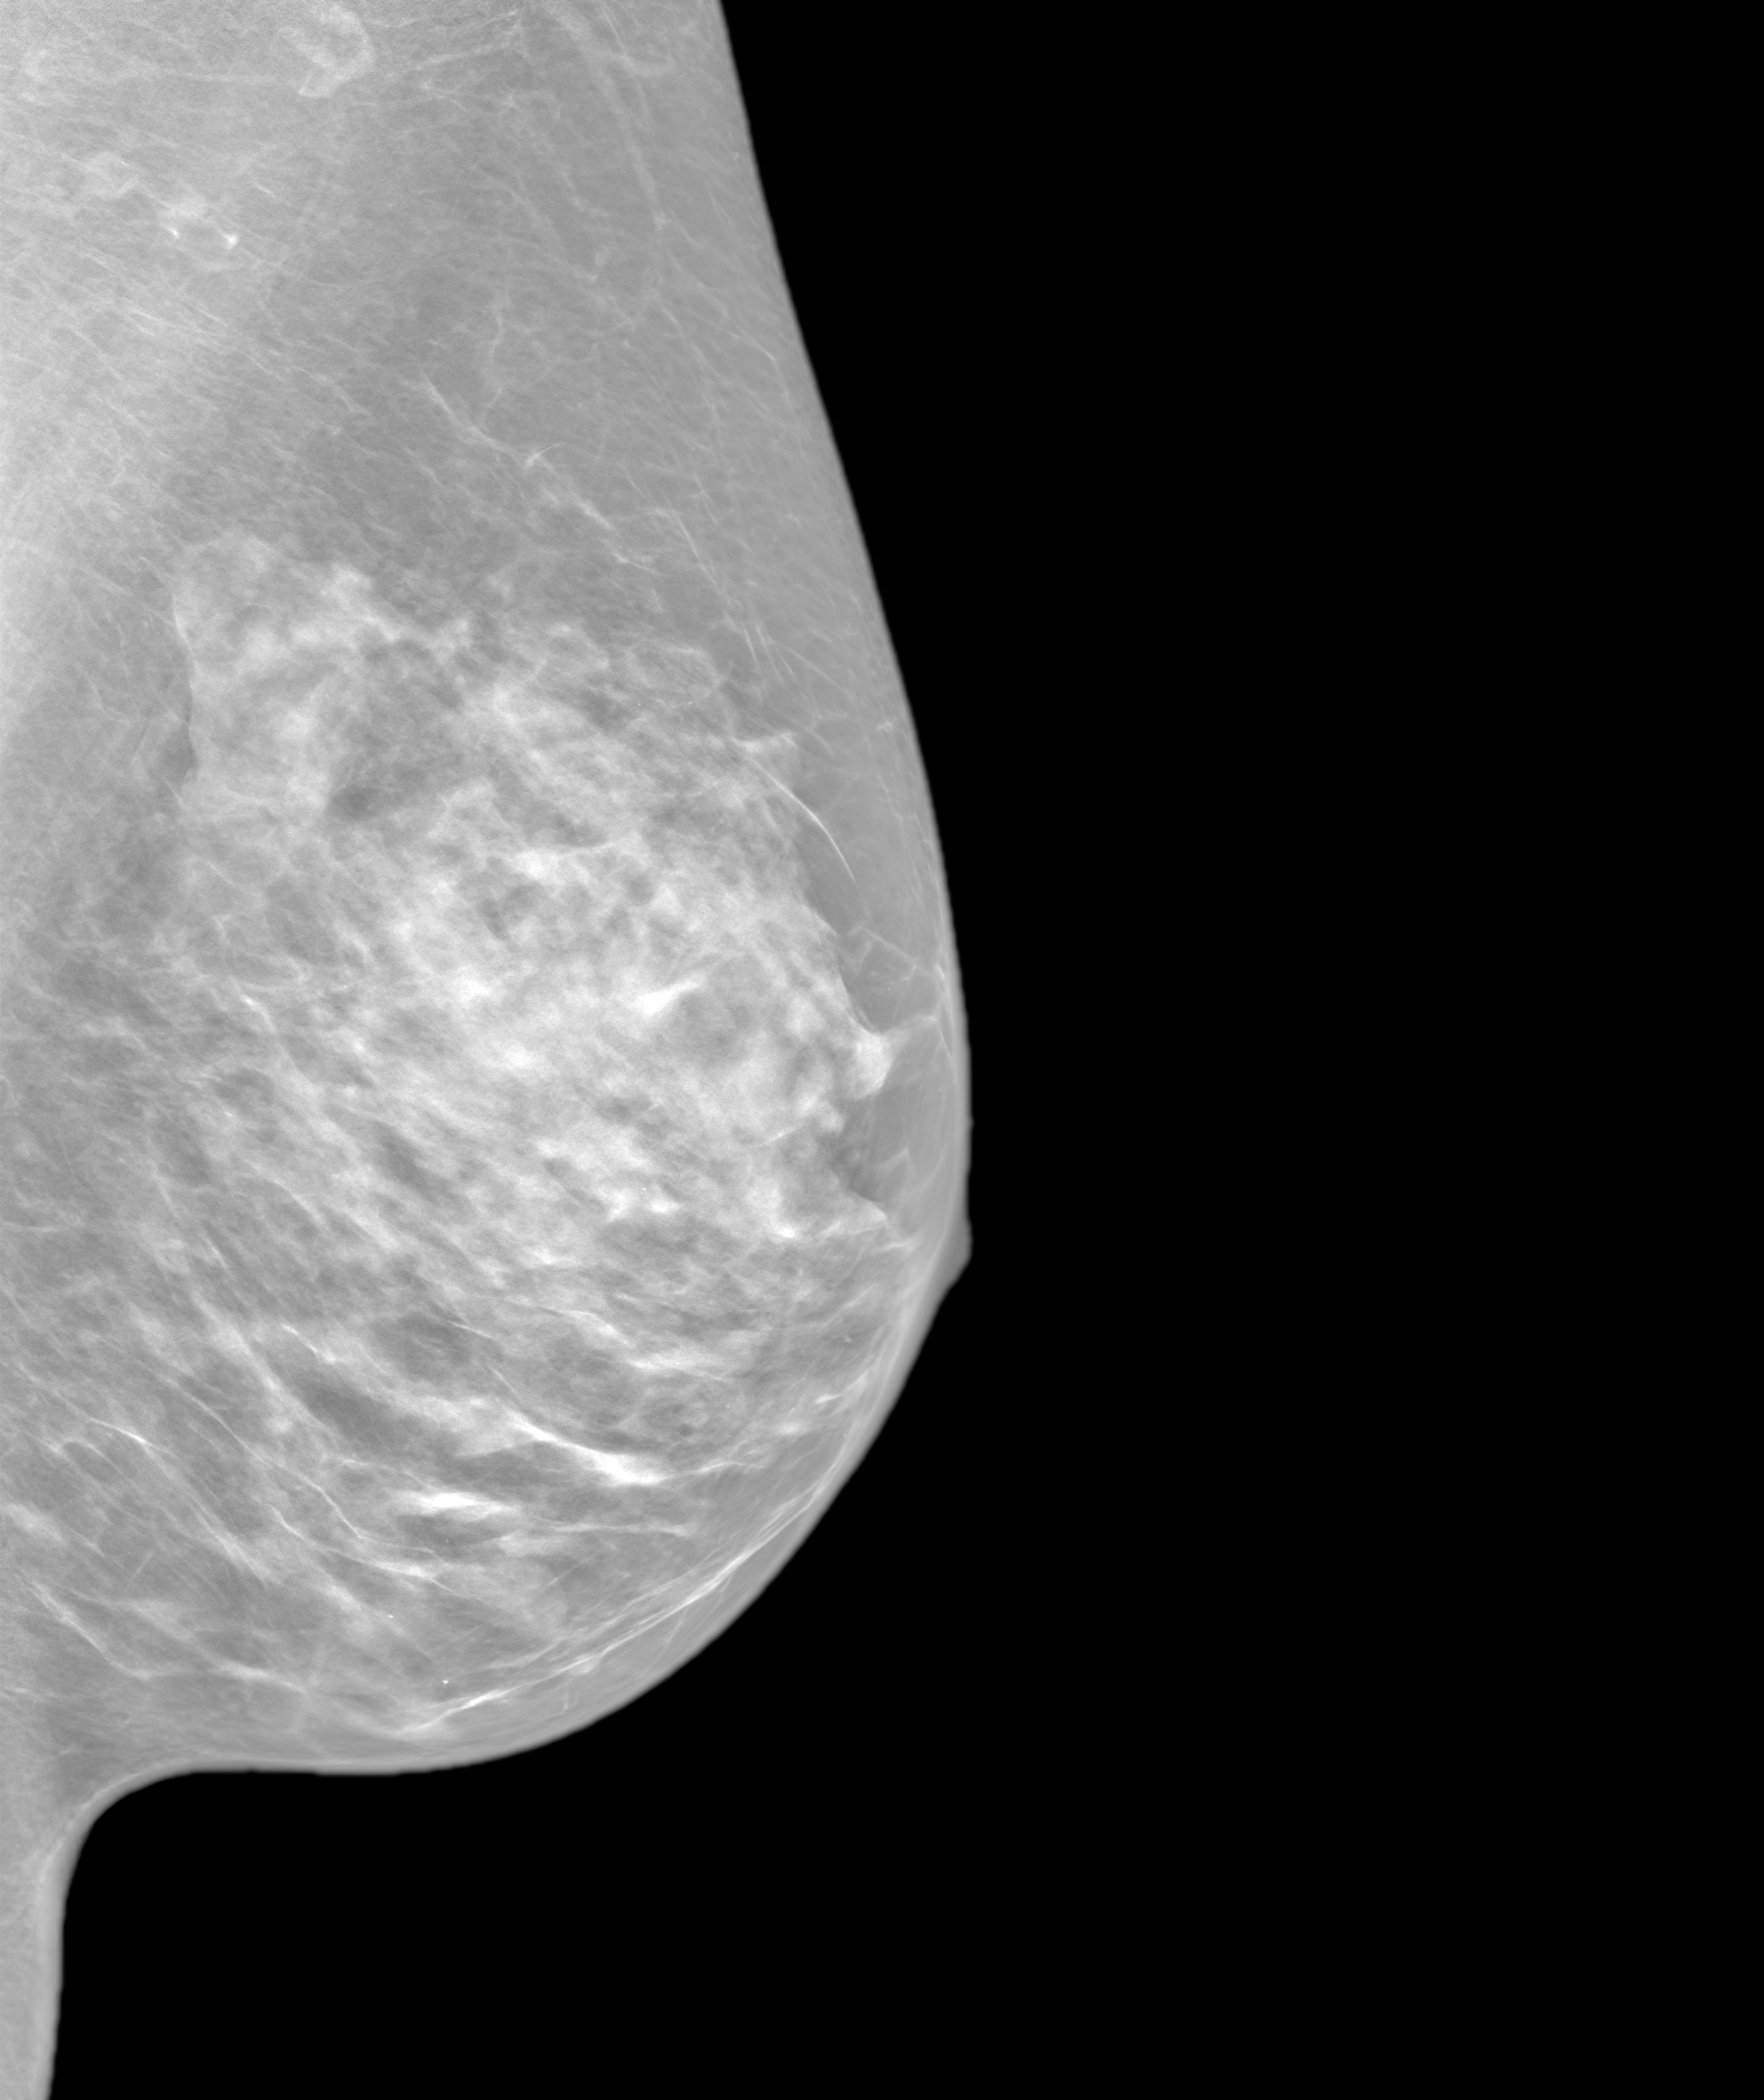
Screening examination; system: SenoIris_1SP1.2(425). Patient aged 65 years (female).
Image type: synthesized 2-D view from tomosynthesis. Breast: left. Projection: medio-lateral oblique projection.